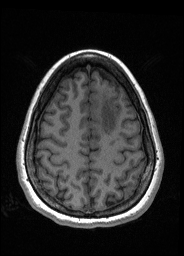
Pre-operative brain MRI before brain-tumour surgery, one axial slice; slice 54 of 176 in the series (ordered by position); T1-weighted post-contrast; 1 mm slice thickness; 184 × 256 image matrix. From the clinical record (not read from this slice): histopathology: Oligodendroglioma; WHO grade: 2; IDH mutation: yes; tumour location: Left Frontal.
Annotated regions visible in this slice (expert manual segmentation):
- tumour: bounding box [x1, y1, x2, y2] px = [92, 95, 118, 135]